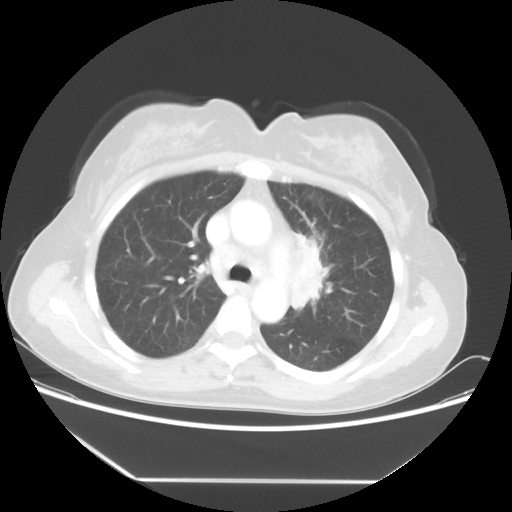
Chest CT, one axial slice. Slice 35 of 52 in the series (ordered by position). Reconstruction kernel STANDARD. 100 kVp. Lung window (W 1500 / L -600 HU). 5 mm slice thickness. 512 × 512 image matrix, field of view 390 × 390 mm. Patient: female, 50 years. From the clinical record (not read from this slice): clinical TNM (as recorded): T2 N3 M0.
Annotated regions visible in this slice (rectangle marked by the reading radiologist):
- lung tumour (recorded histology: adenocarcinoma): bounding box (x1, y1, x2, y2) in pixels: (285, 221, 338, 324)